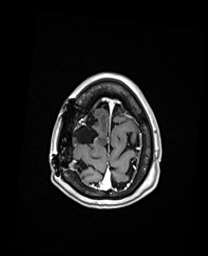
Brain MRI from a brain-tumour surgery series, one axial slice. Slice 32 of 192 in the series (ordered by position). T1-weighted post-contrast. 1 mm slice thickness. 208 × 256 image matrix, field of view 208 × 256 mm. From the clinical record (not read from this slice): histopathology: Oligodendroglioma; WHO grade: 3; IDH mutation: yes.
Outlined on this slice (outlined manually by an expert reader):
- previous resection cavity: box from (x=72, y=113) to (x=99, y=143) px